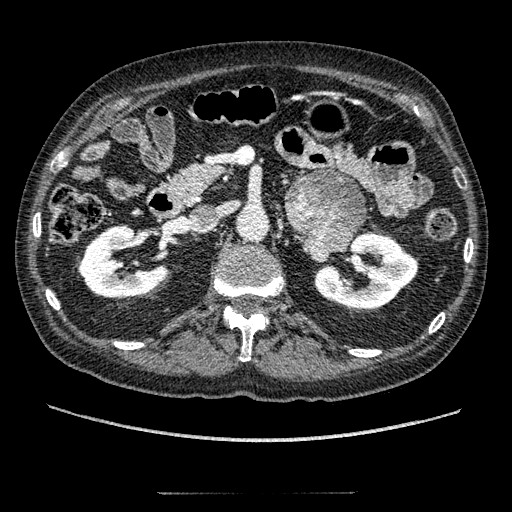
Contrast-enhanced abdominal CT, one axial slice; position 103 of 274 along the scan axis; intravenous contrast given; soft-tissue window (W 400 / L 40 HU); 1.25 mm slice thickness; 512 × 512 image matrix. Male patient, age 69 years. From the clinical record (not read from this slice): diagnosis: adrenocortical carcinoma; tumour side: left adrenal; tumour size at pathology: 6.1 cm; Ki-67 index: 10 %; stage (as recorded): 3.
Outlined on this slice (semi-automatically segmented with operator editing):
- mass: bounding box <287,171,366,260> (left, top, right, bottom; pixels)